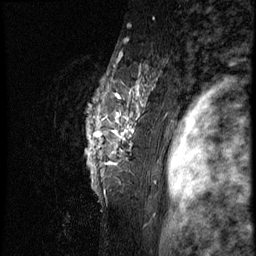
Breast MRI (dynamic contrast-enhanced), one sagittal slice; 3 images stored at this slice position (order not interpretable as contrast timing); 1.5 T; TE 4.2 ms, TR 8.9 ms; 2.5 mm slice thickness; 256 × 256 image matrix, field of view 200 × 200 mm. Patient: female, 39 years. Case-level facts recorded for this patient, not image findings: setting: breast cancer imaged before/during neoadjuvant chemotherapy; receptor status: HER2-positive.
Structures marked on this image (semi-automatically segmented with operator editing):
- analysis volume of interest (the breast-tissue region the enhancement analysis was run in; not a lesion): bounding box <74,44,166,196> (left, top, right, bottom; pixels)
- tumour enhancement mask (voxels above the 140 % enhancement threshold inside the analysis volume of interest): <113,80,140,144>